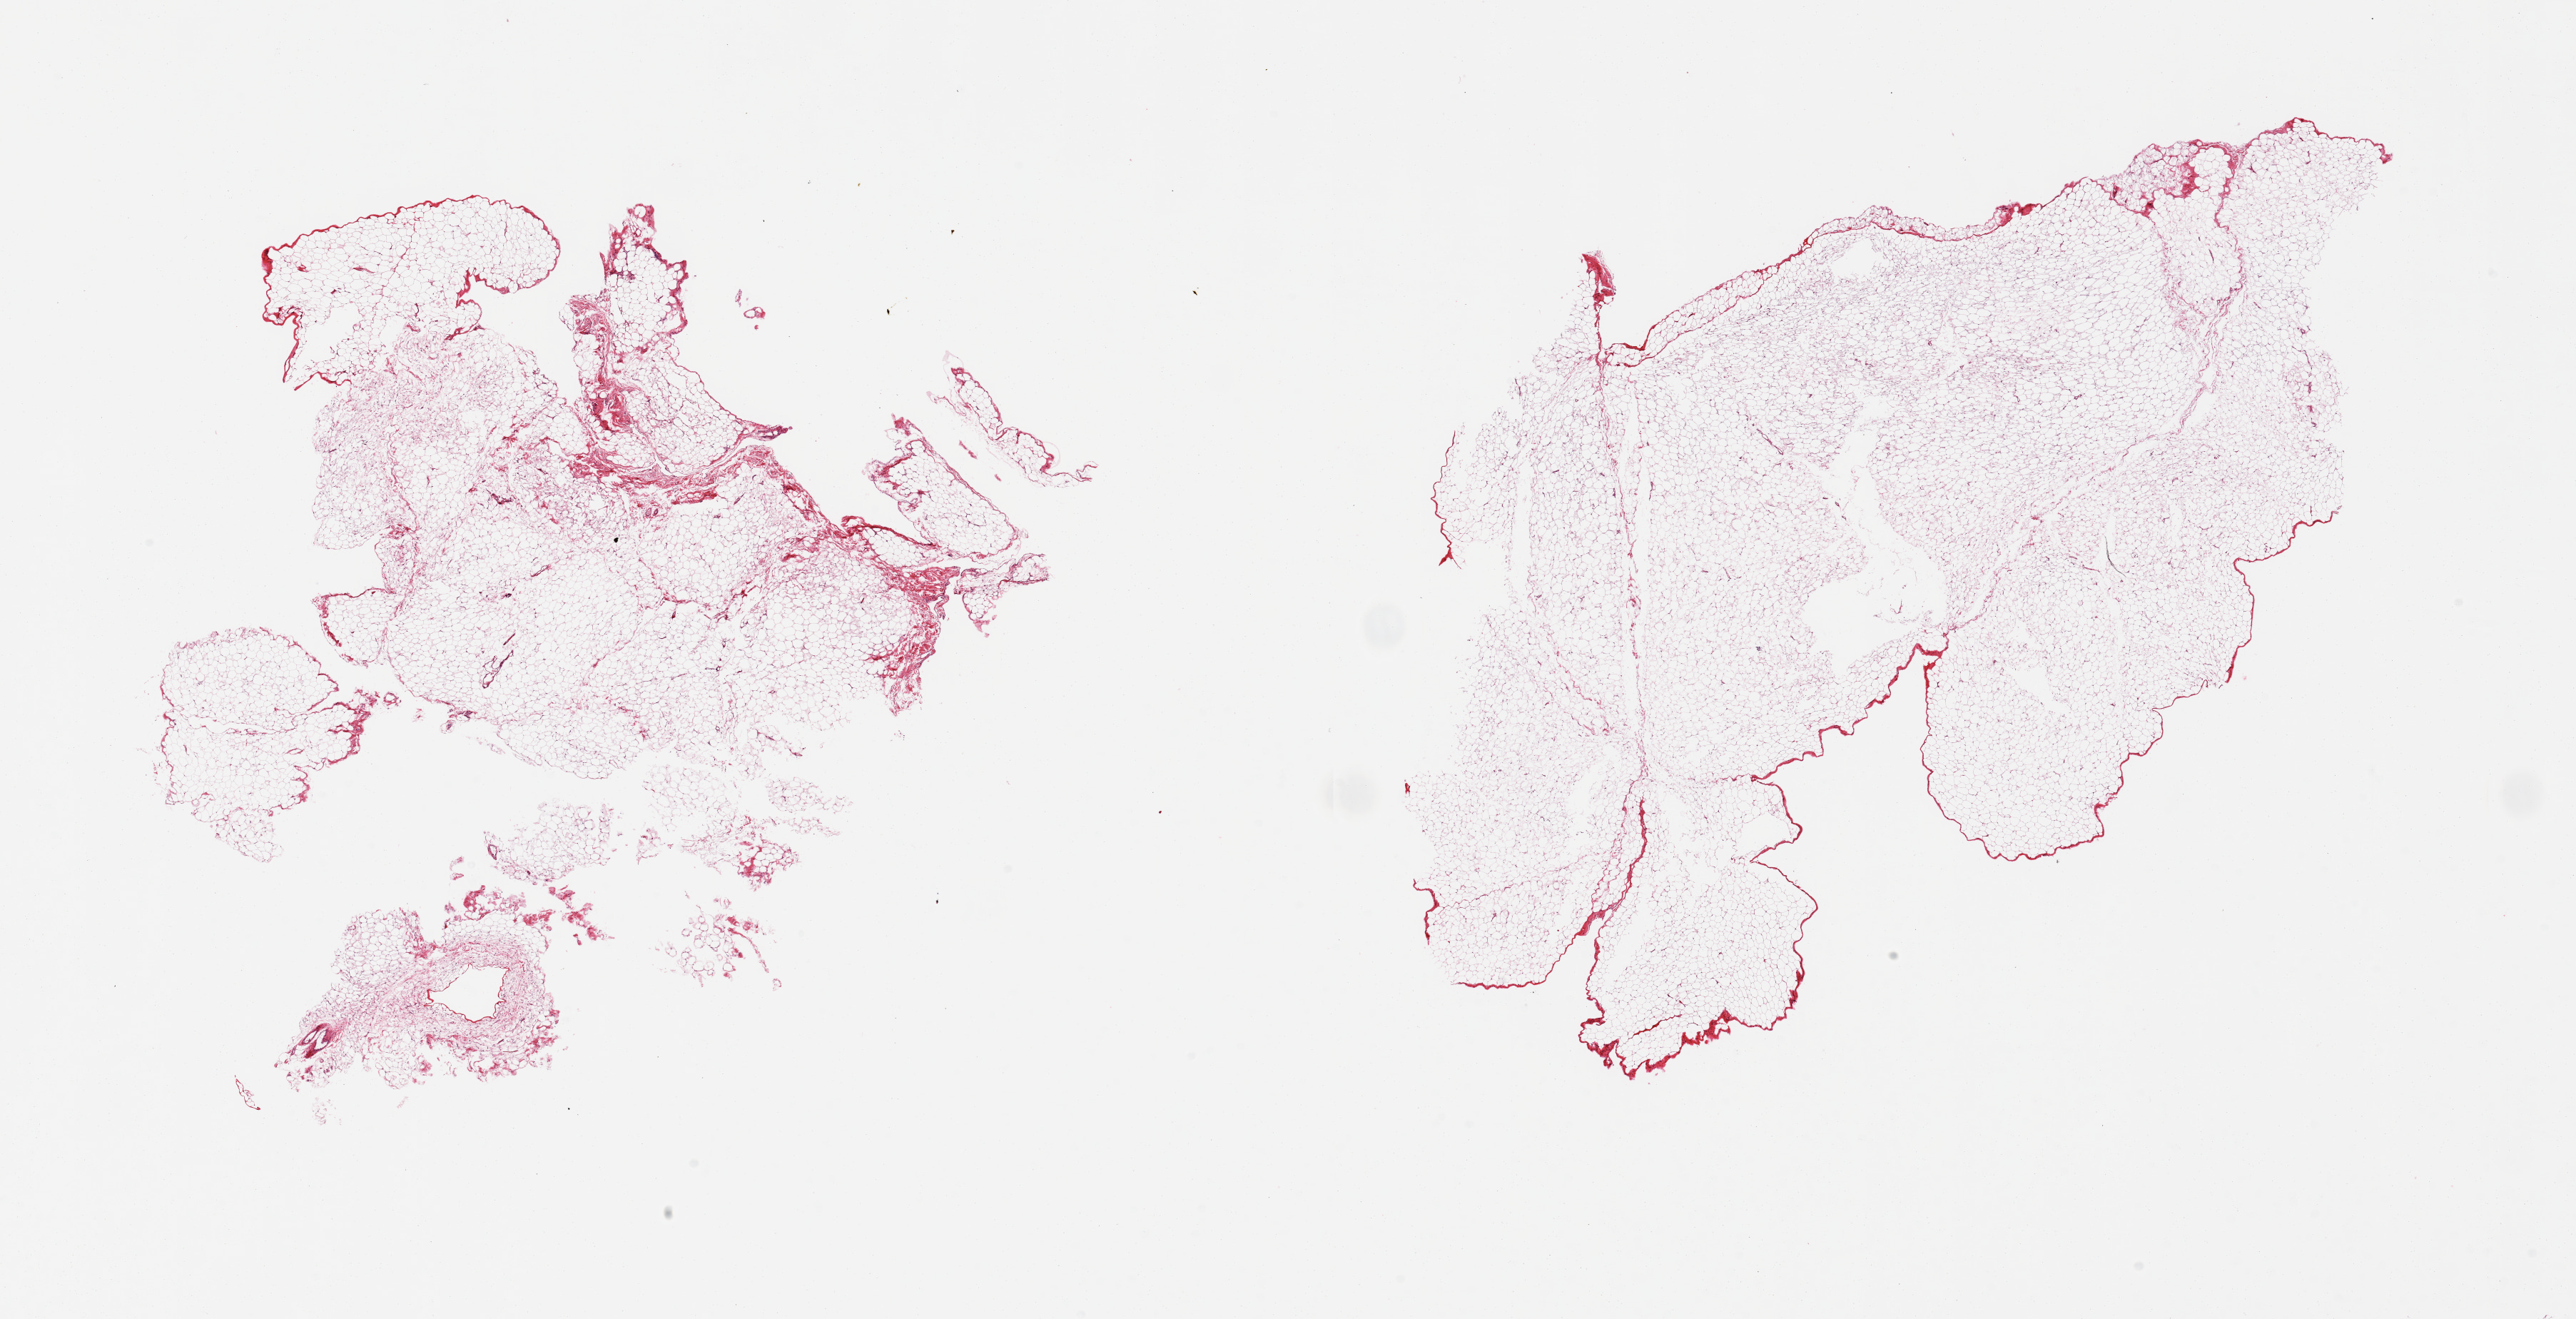
Digitized haematoxylin and eosin-stained section, brightfield, shown as a low-resolution overview of the whole scanned area (about 28.5 x 14.6 mm); PAXgene-fixed paraffin-embedded (PFPE) section; sampled site (target tissue): omentum; tissue donor sample. Male donor.
Reviewer comment on this tissue sample: 2 pieces (one fragmented); lobulated mature adipose tissue with less than 5% fibrovascular component.